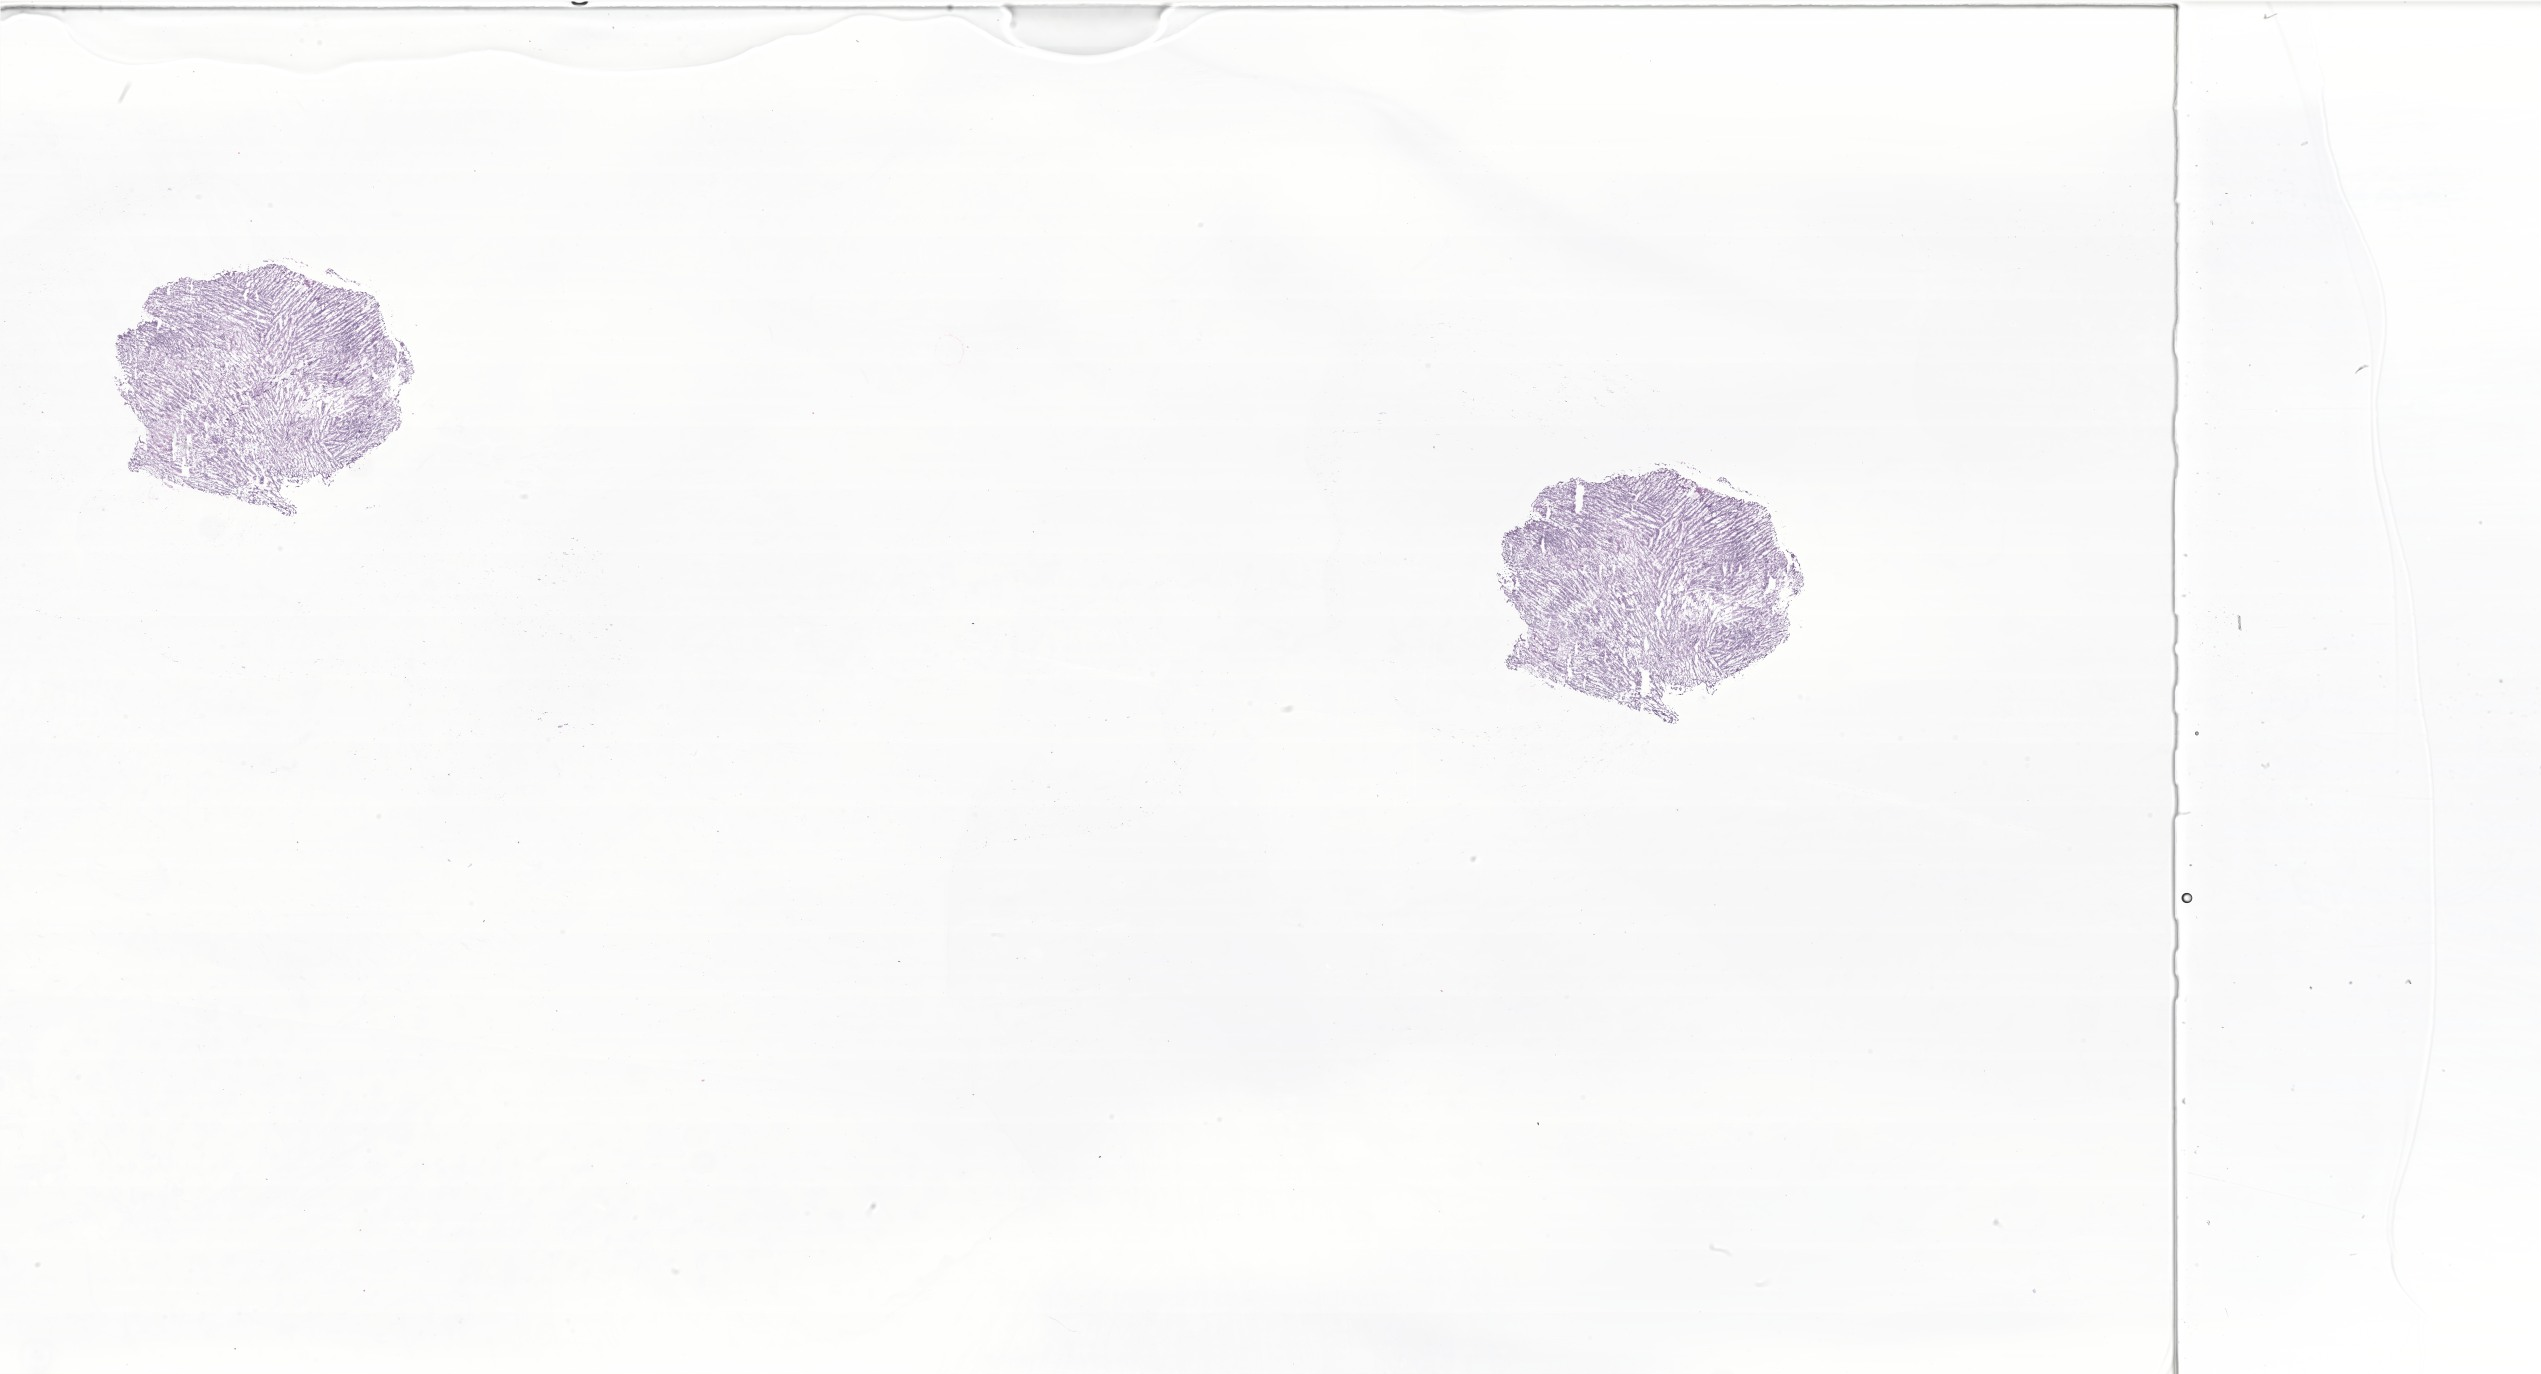
Hematoxylin and eosin (H&E) whole-slide image of tumor tissue from the retroperitoneum, shown as a low-resolution overview of the whole scanned area (about 42.9 x 23.2 mm). Frozen section (OCT-embedded). Female patient, age 123 months.
* recorded diagnosis: Neuroblastoma, NOS